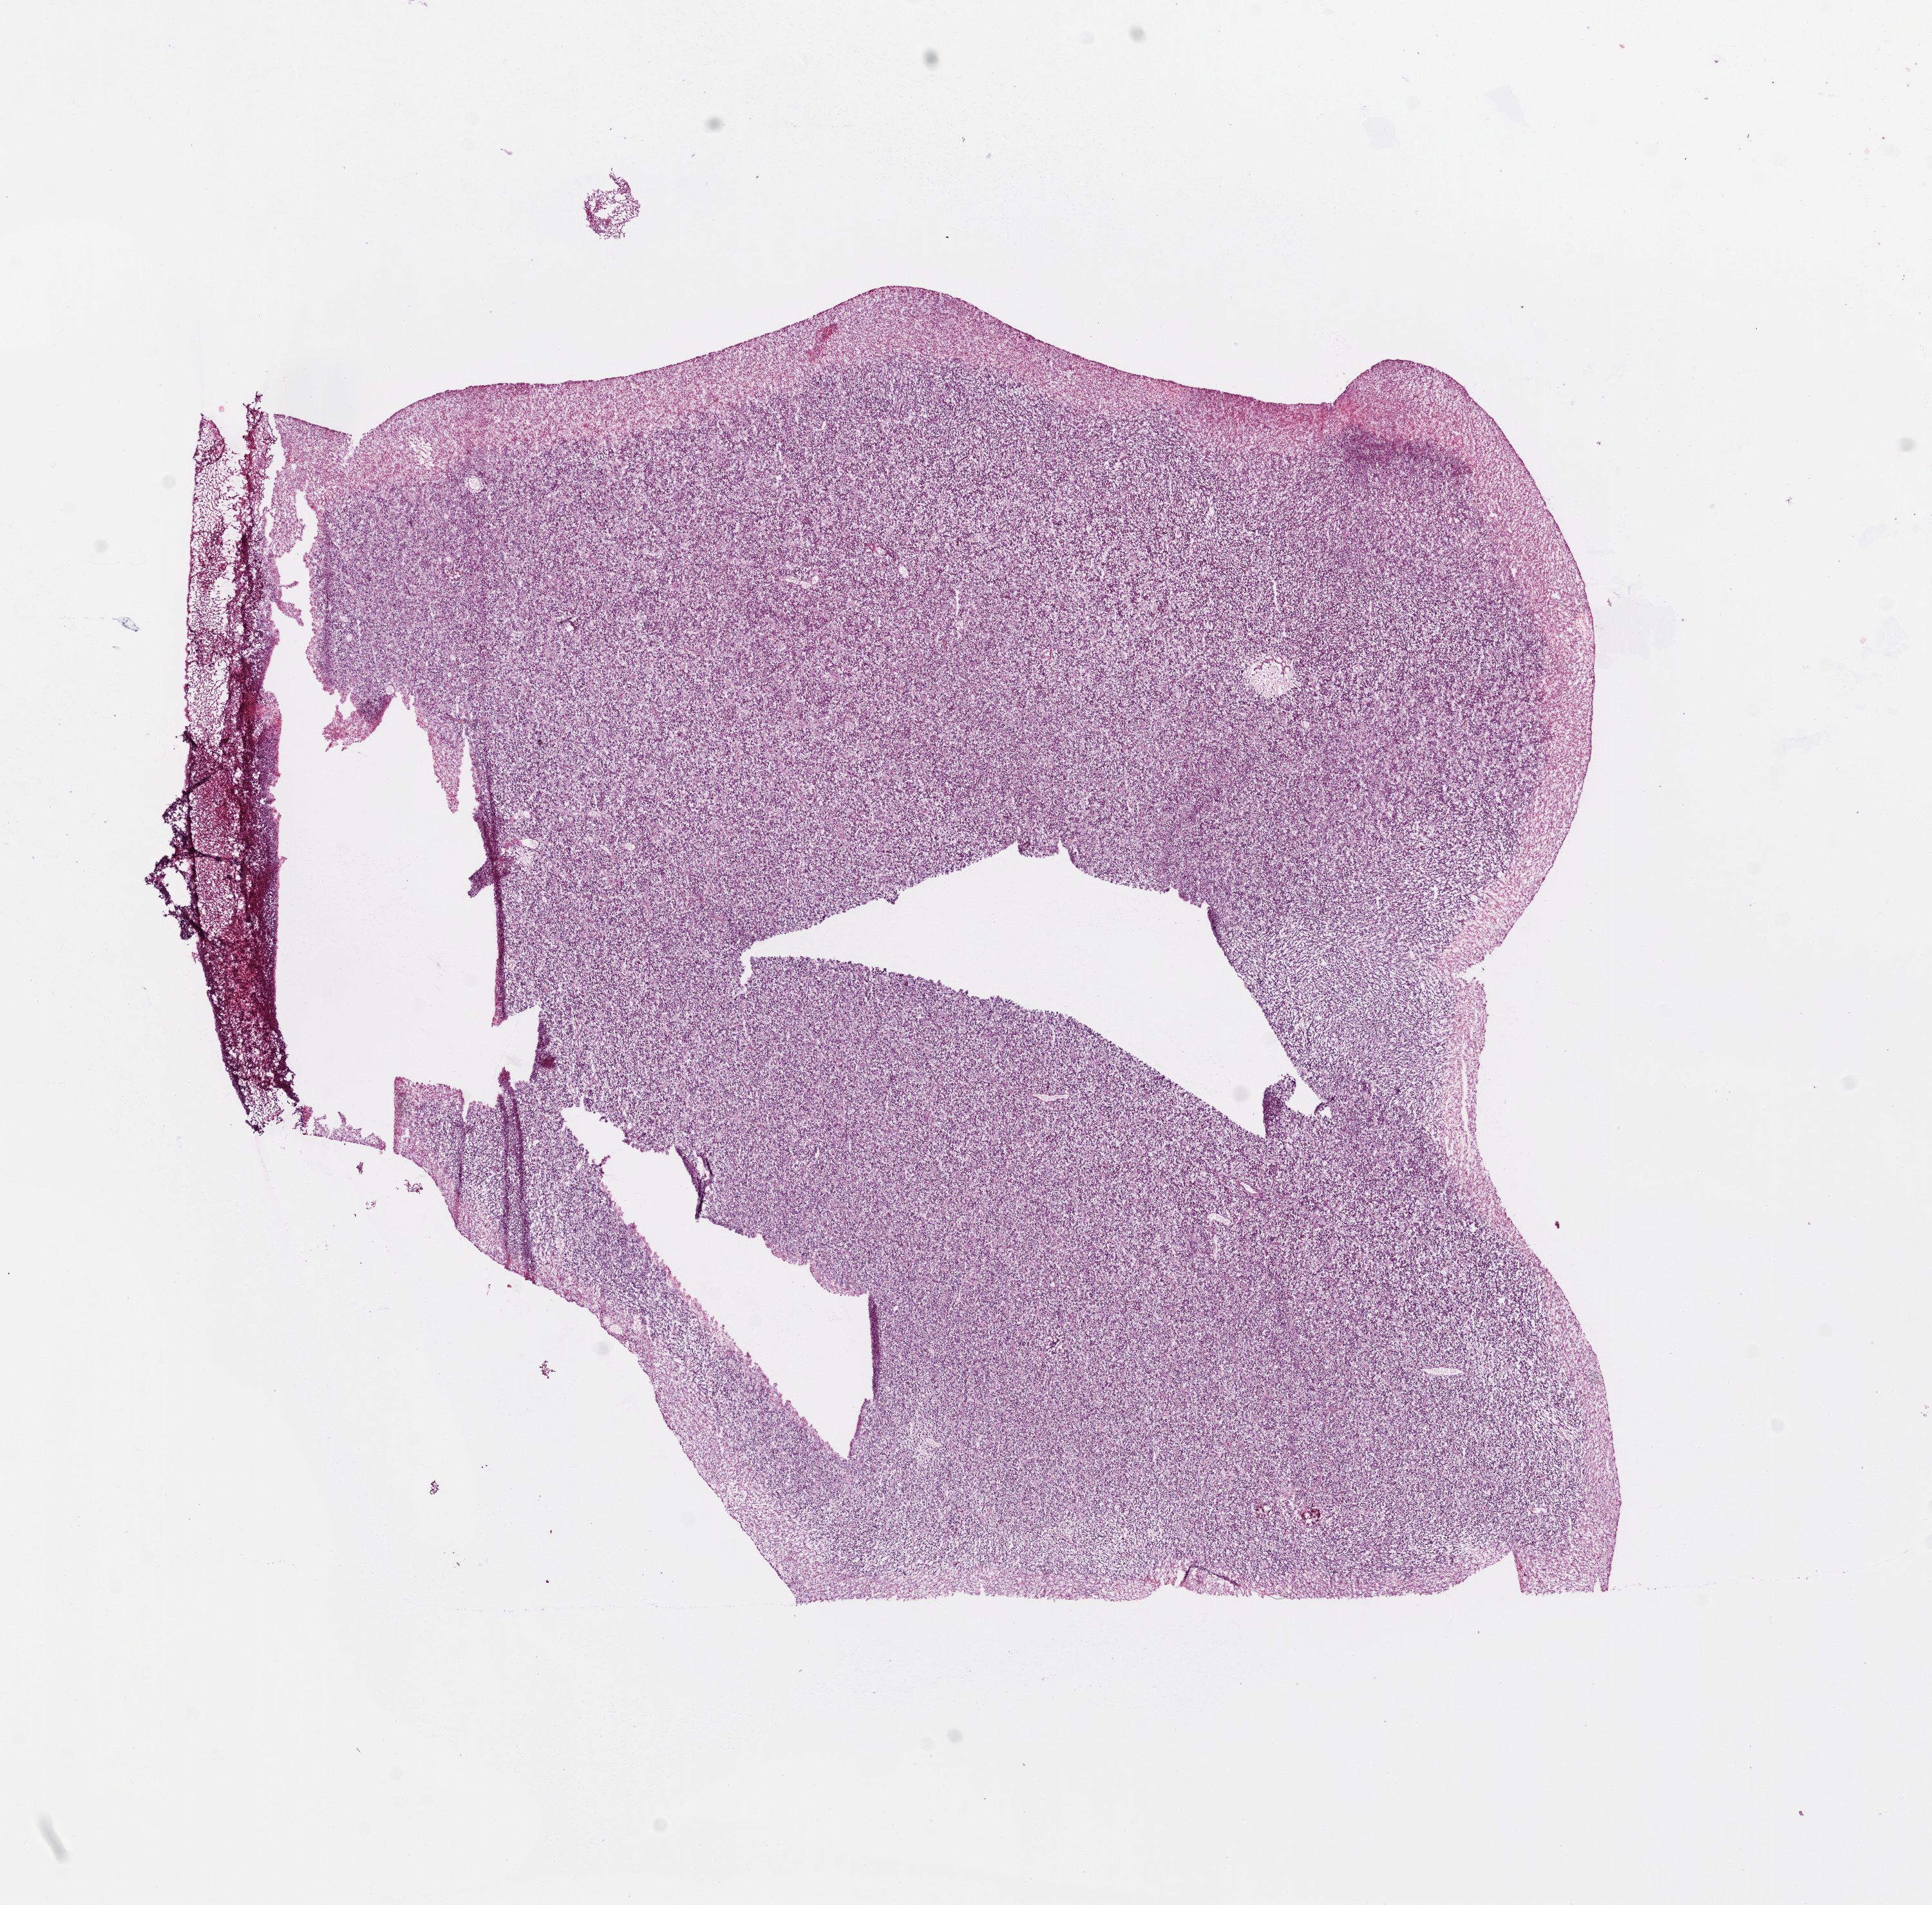
Whole-slide histology image, H&E, a low-resolution overview of the entire scanned area, about 12.0 x 11.9 mm. Frozen section. Primary tumour sample from the brain. Female, age 34 years at initial diagnosis. Composition of this section per pathologist review: tumour cells 99%, tumour nuclei 85%, normal cells 0%, stromal cells 0%, necrosis 1%.
- pathologic diagnosis: Glioblastoma